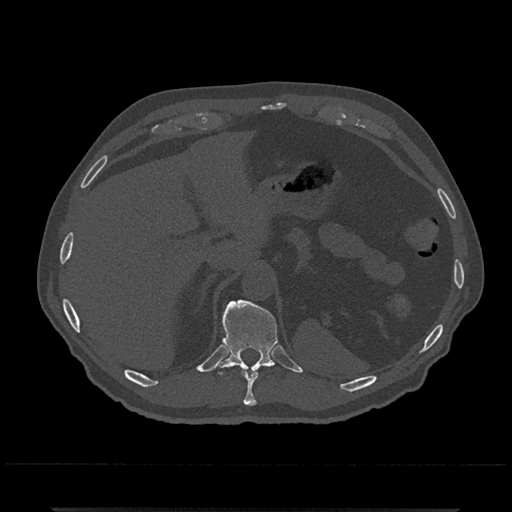
CT including the spine, one axial slice; position 512 of 797 along the scan axis; reconstruction kernel Br40s/3; 120 kVp; bone window (W 1800 / L 400 HU); 0.5 mm slice thickness; 512 × 512 image matrix, field of view 393 × 393 mm. Patient: male, 67 years. Case-level facts recorded for this patient, not image findings: primary cancer: prostate.
Structures marked on this image (semi-automatic segmentation, software-assisted and operator-edited):
- T10 vertebra: bounding box [x1, y1, x2, y2] px = [242, 371, 258, 406]
- T11 vertebra: [216, 300, 278, 376]